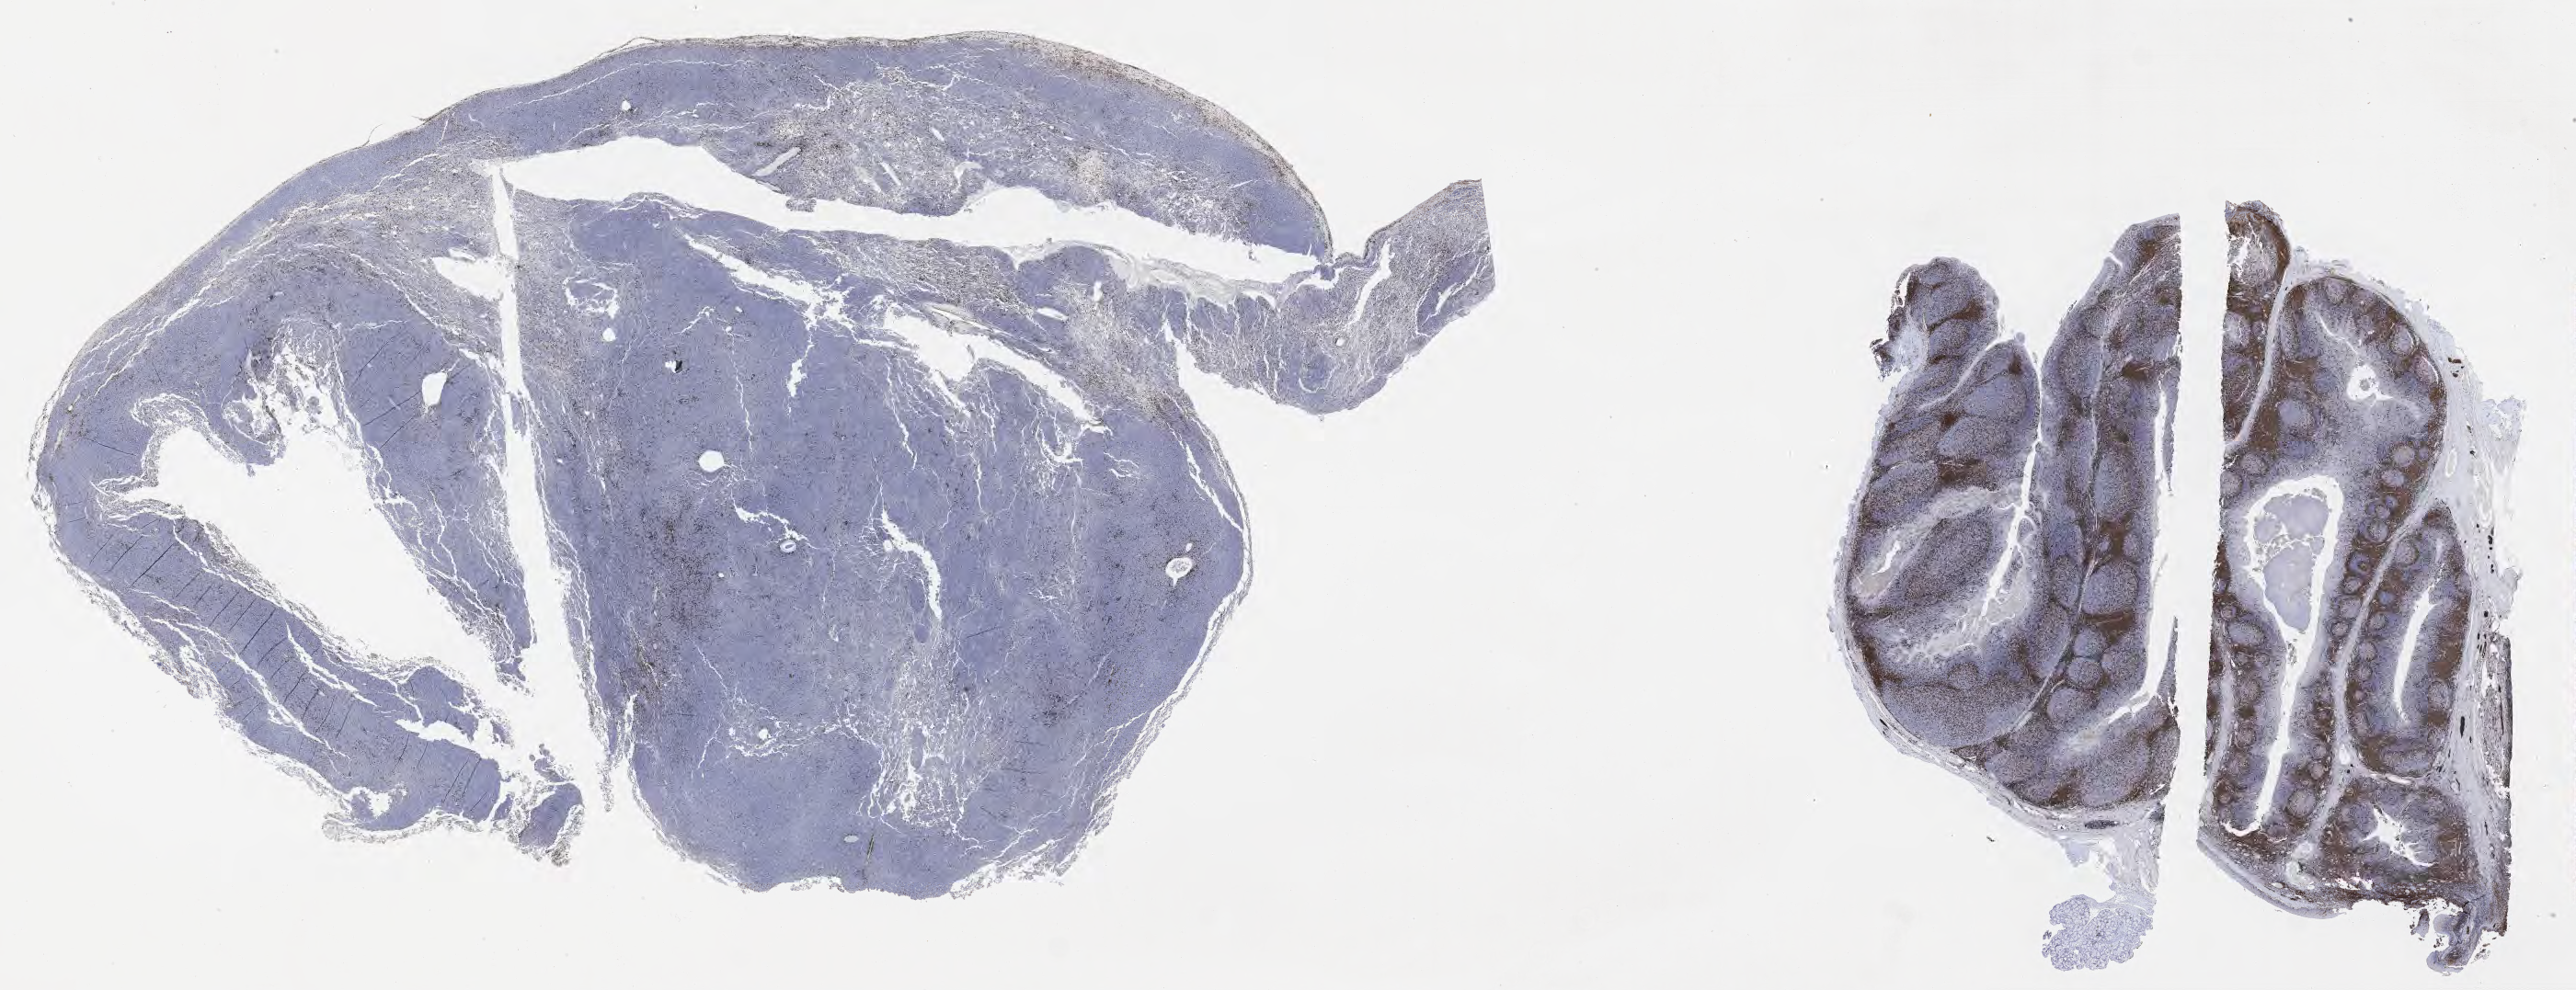
Whole-slide image, immunohistochemical stain for CD3 — a low-resolution overview of the entire scanned area, about 45.3 x 17.4 mm, tumor tissue. Patient: female, age at initial diagnosis 3 years.
* histologic diagnosis: Burkitt lymphoma, NOS